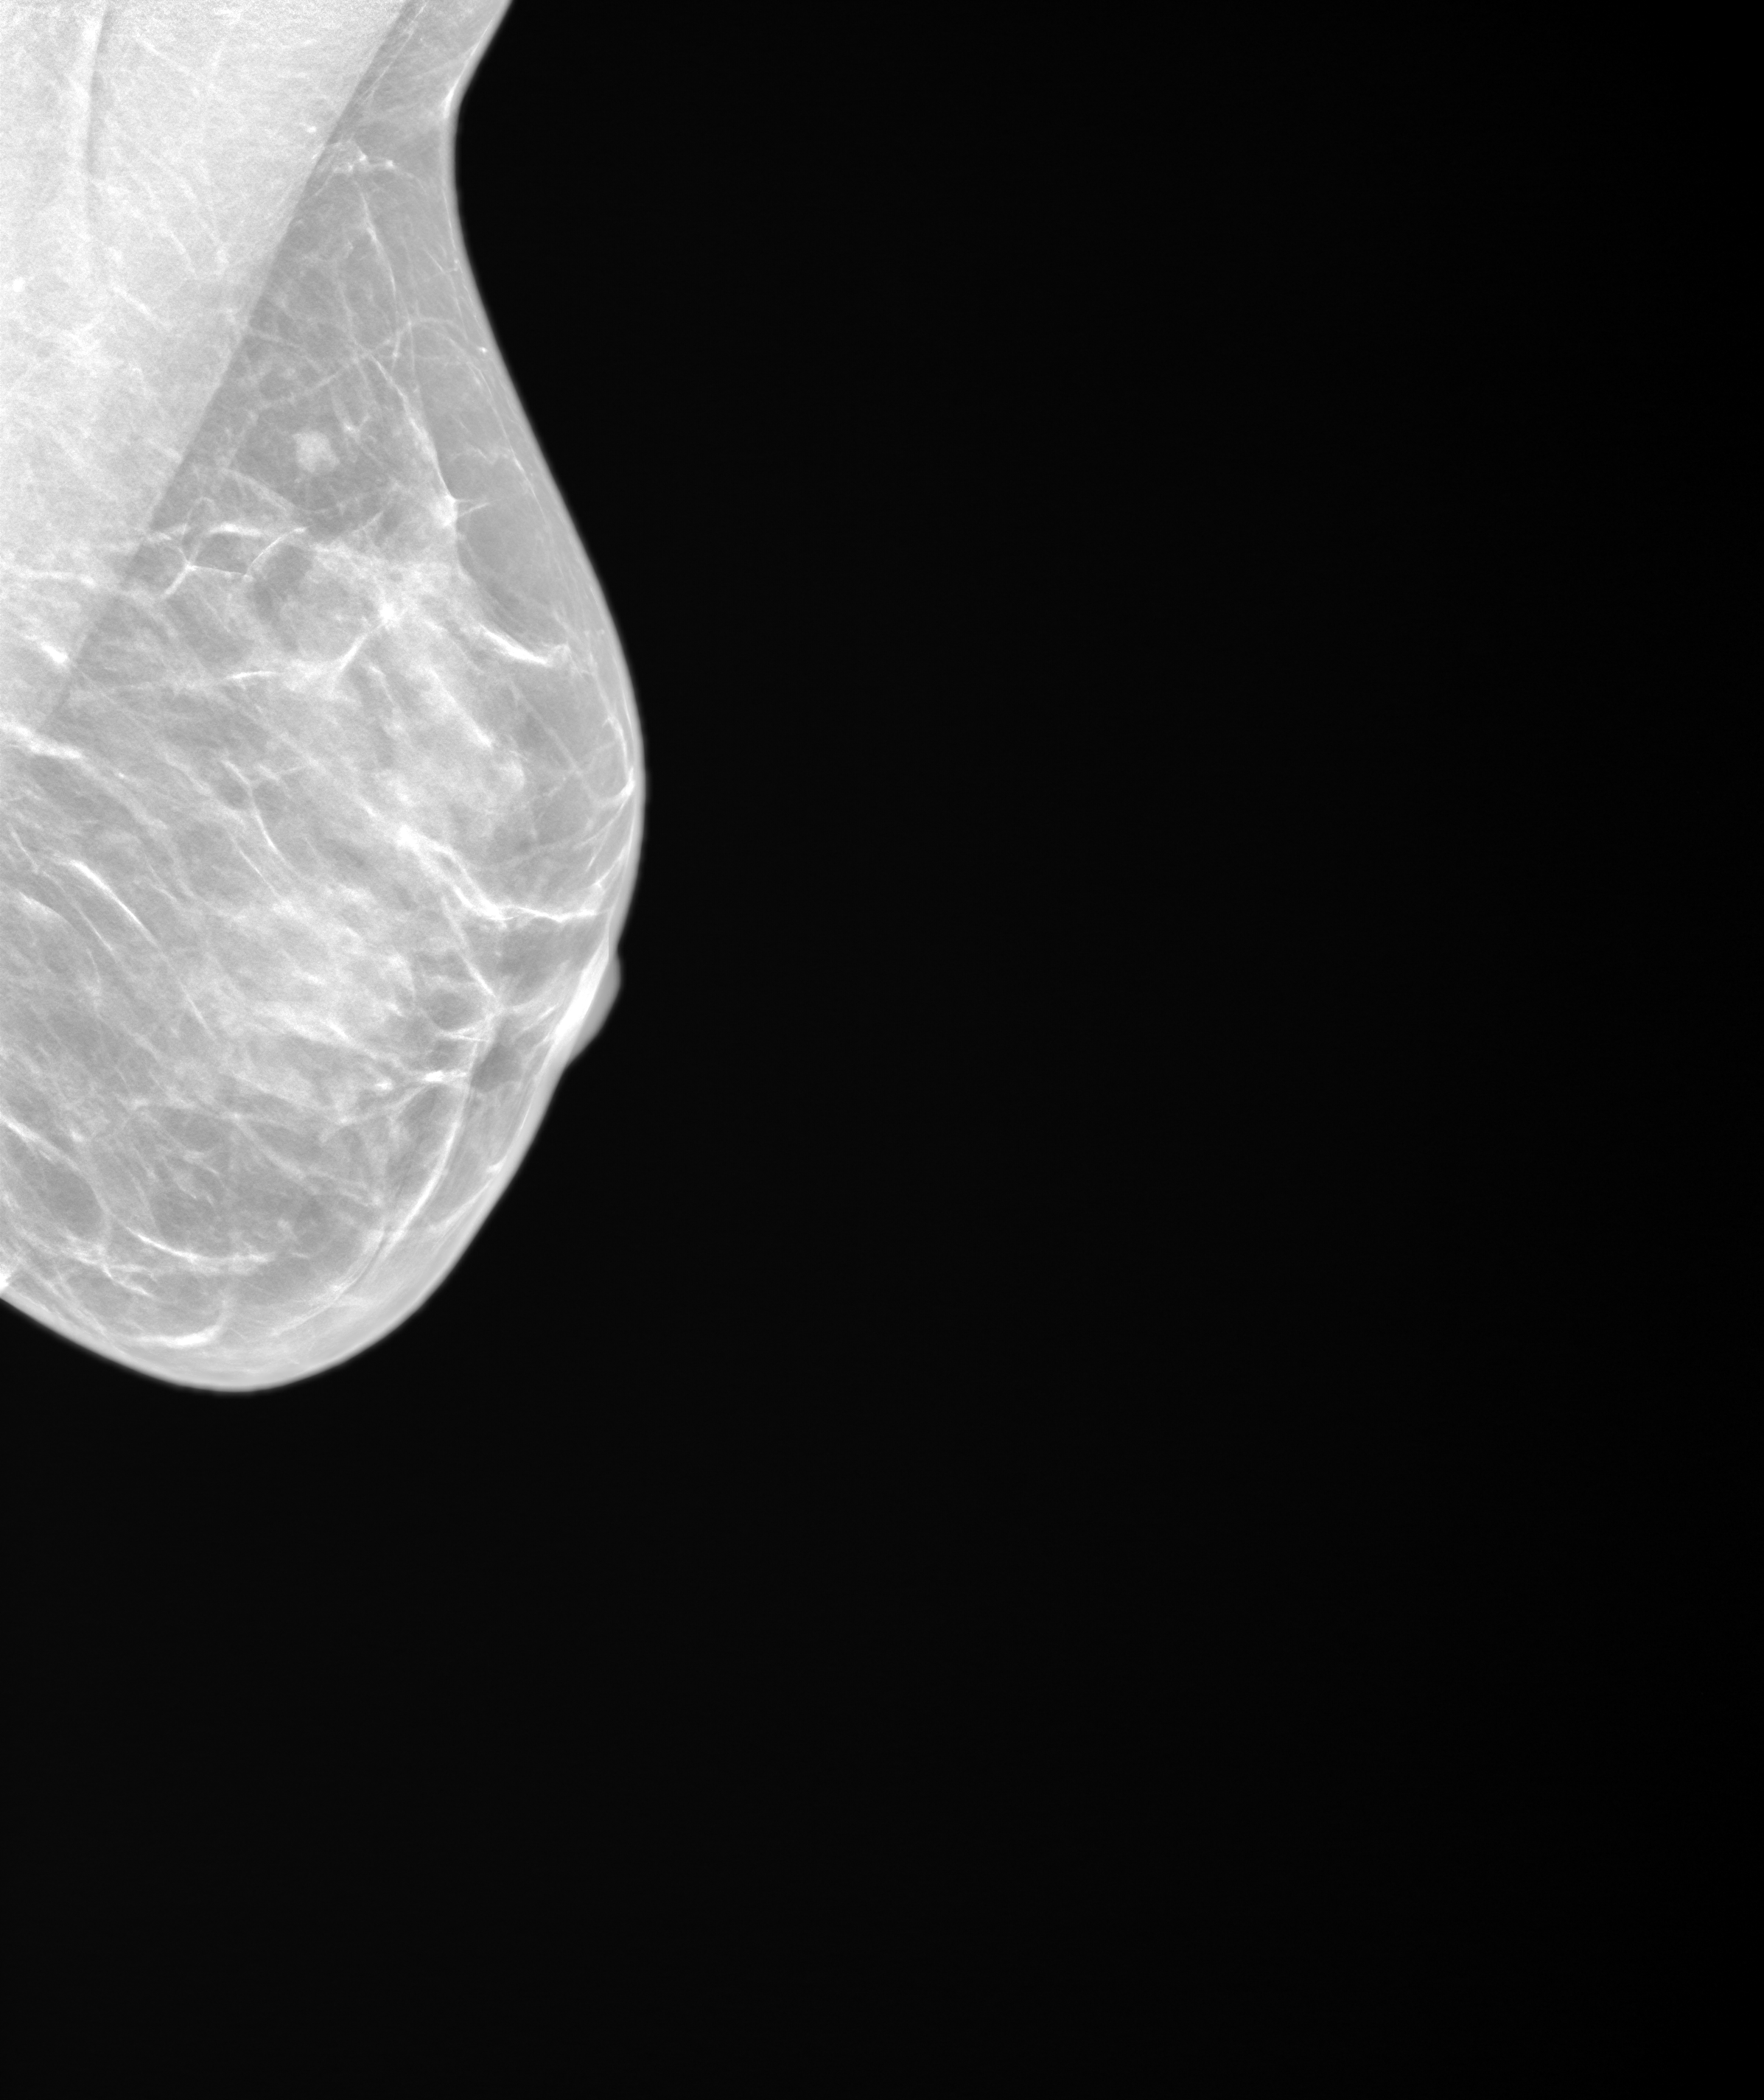
Synthetic 2-D view generated from a tomosynthesis acquisition (not an FFDM exposure); left breast; MLO view; annual screening mammography examination. Patient aged 47 years (female).
Breast density at the screening exam (both breasts): heterogeneously dense (BI-RADS density category c). Final BI-RADS category for the screening round (tomosynthesis exam, both breasts): category 2. Recall: no recall after this screen.